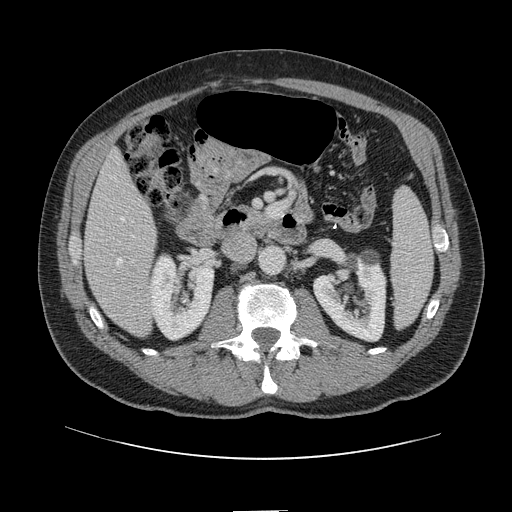
Contrast-enhanced abdominal CT, one axial slice. Position 42 of 161 along the scan axis. 120 kVp. Intravenous contrast given. Soft-tissue window (W 400 / L 40 HU). 512 × 512 image matrix, field of view 412 × 412 mm. Male patient, age 66 years. Case-level facts recorded for this patient, not image findings: diagnosis: colorectal cancer liver metastases, imaged before liver resection; multiple liver metastases: no; largest metastasis: 3.5 cm.
Annotated regions visible in this slice (expert manual segmentation):
- hepatic veins: bounding box <117,217,125,265> (left, top, right, bottom; pixels)
- liver: <85,153,156,337>
- planned liver remnant (the part of the liver to remain after resection): <85,153,153,271>